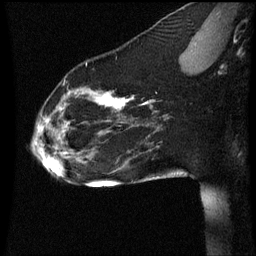
Breast MRI (dynamic contrast-enhanced), one sagittal slice; dynamic contrast-enhanced series, image 2 of 3 at this slice position (ordered by acquisition); 1.5 T; TE 4.2 ms, TR 8.9 ms; 2 mm slice thickness; 256 × 256 image matrix, field of view 200 × 200 mm. Patient: female, 35 years. From the clinical record (not read from this slice): setting: breast cancer imaged before/during neoadjuvant chemotherapy; receptor status: HER2-positive.
Outlined on this slice (semi-automatic segmentation, software-assisted and operator-edited):
- analysis volume of interest (the breast-tissue region the enhancement analysis was run in; not a lesion): box from (x=30, y=66) to (x=177, y=177) px
- tumour enhancement mask (voxels above the 70 % enhancement threshold inside the analysis volume of interest): (x=48, y=92)–(x=149, y=155)